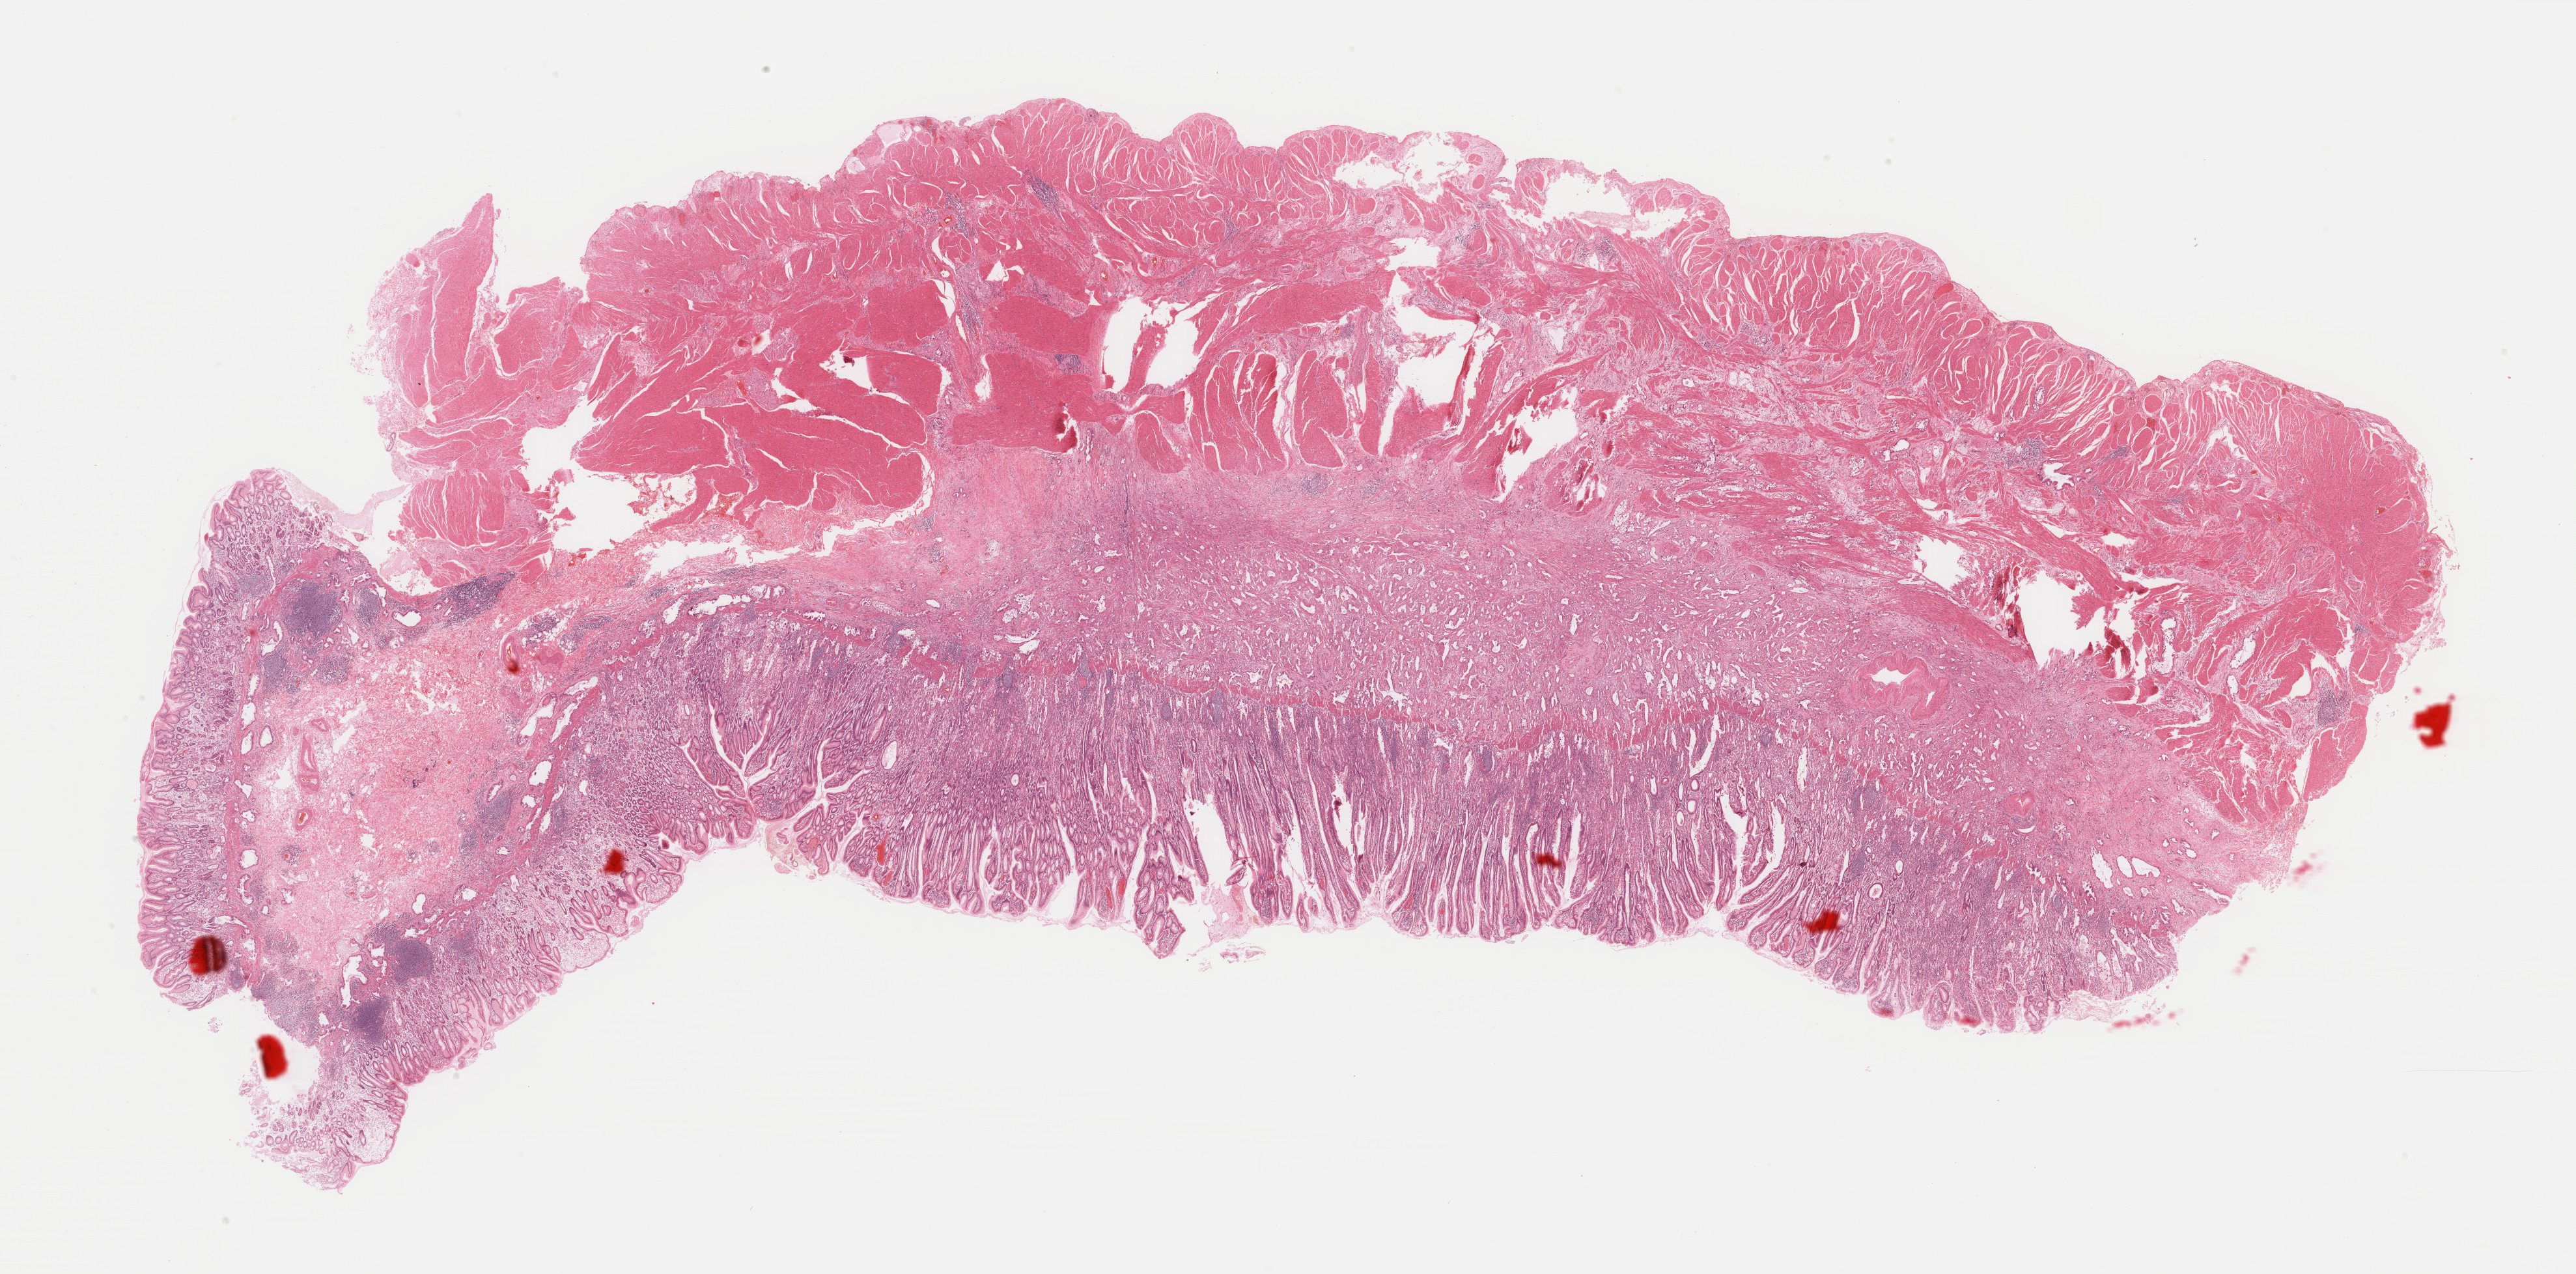
Whole-slide histology image, H&E-stained, low-resolution overview of the scanned area, about 31.4 x 15.5 mm; formalin-fixed paraffin-embedded (FFPE) diagnostic section; primary tumour sample from the pancreas. Patient: male, age at initial diagnosis 74 years. Histologic grade: G3 (poorly differentiated).
AJCC pathologic stage: IB (7th edition). Pathologic diagnosis: Infiltrating duct carcinoma, NOS (head of pancreas).